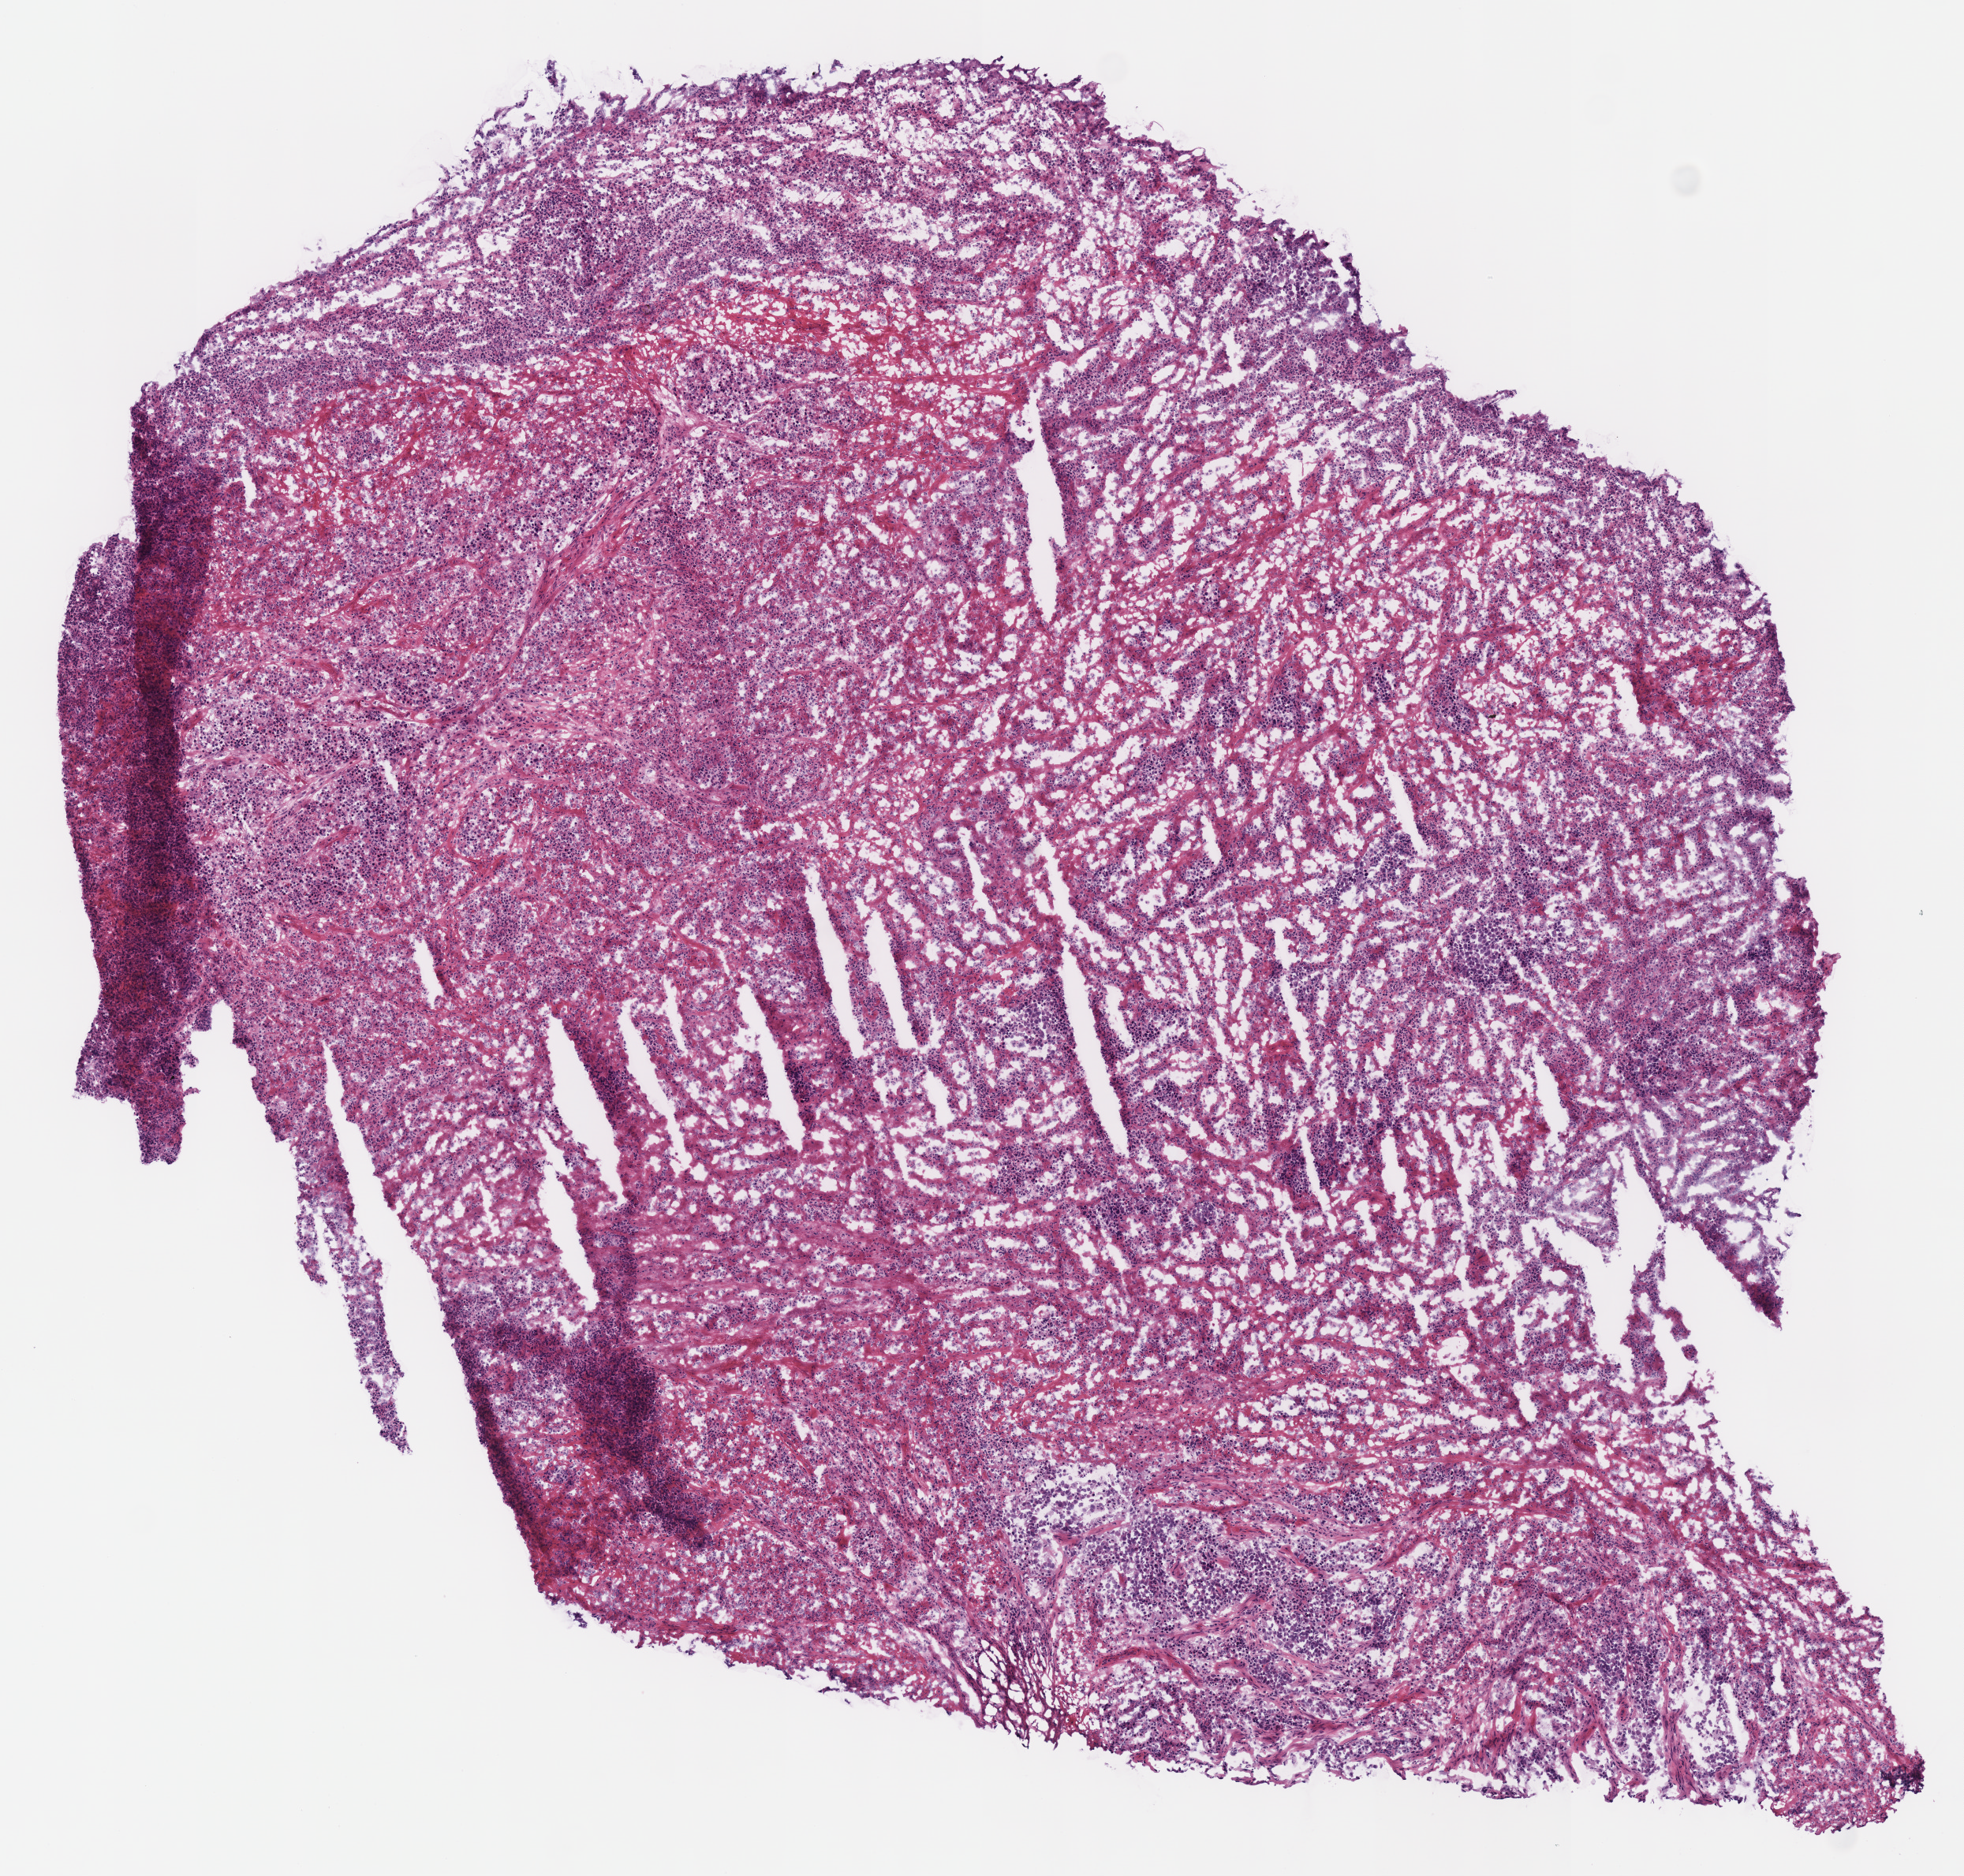
Hematoxylin and eosin (H&E) stained whole-slide image, low-resolution overview of the scanned area, about 4.9 x 4.7 mm (acquisition: 40x scan). Frozen section from the top of the tissue portion. Stomach, primary tumour sample. Patient: female, age at initial diagnosis 58 years. Histologic grade: G3 (poorly differentiated). Composition of this section per pathologist review: tumour cells 90%, tumour nuclei 65%, normal cells 0%, stromal cells 10%, necrosis 0%.
Diagnosis: Carcinoma, diffuse type (gastric antrum). Lymph nodes positive (case pathology): 0 of 61 examined. TNM: T4a N0 M0. AJCC pathologic stage: IIB (7th edition).